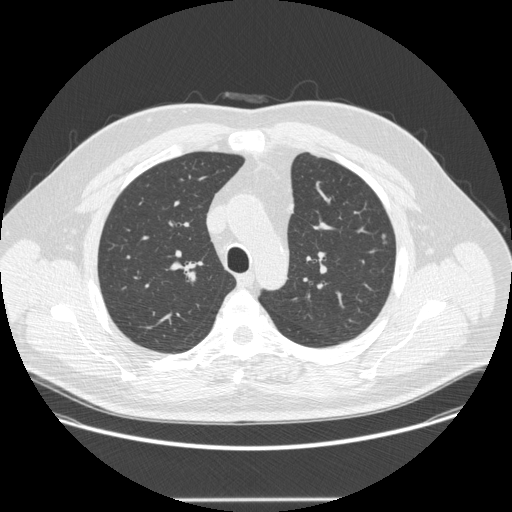
Chest CT (low-dose screening protocol), one axial image; baseline annual screen; lung window (W 1500 / L -600 HU); standard (soft-tissue) reconstruction kernel (STANDARD); slice 67 of 252 in the series; 512 × 512 image matrix. Male participant, aged 55 years at enrolment.
Expert reader's lesion annotation, bounding box <373,228,403,254> (left, top, right, bottom; pixels). The exam's reader record, not a measurement of the box and not confirmed to be the same lesion: non-calcified nodule or mass ≥4 mm, left upper lobe, 5 × 4 mm, smooth margins, soft tissue attenuation. Official screen result: positive, change unspecified: nodule(s) >= 4 mm or enlarging nodule(s), mass(es), or other non-specific abnormalities suspicious for lung cancer. Participant outcome: lung cancer diagnosed 462 days after this screen (after the second annual screen) — adenocarcinoma, NOS, left upper lobe, moderately differentiated (G2), stage IA (AJCC 6th edition), 9 mm at pathology.